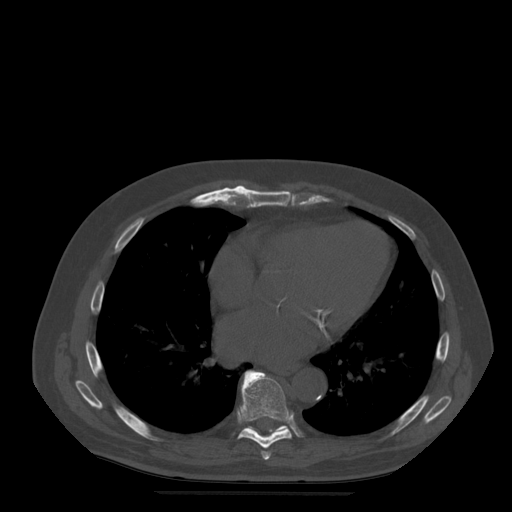
CT including the spine, one axial slice; position 308 of 522 along the scan axis; bone window (W 1800 / L 400 HU); 1.25 mm slice thickness; 512 × 512 image matrix, field of view 420 × 420 mm. Patient age 72 years. Case-level facts recorded for this patient, not image findings: primary cancer: prostate.
Outlined on this slice (semi-automatically segmented with operator editing):
- T7 vertebra: bounding box (x1, y1, x2, y2) in pixels: (262, 451, 271, 460)
- T8 vertebra: (238, 371, 292, 449)
- T9 vertebra: (245, 371, 289, 433)